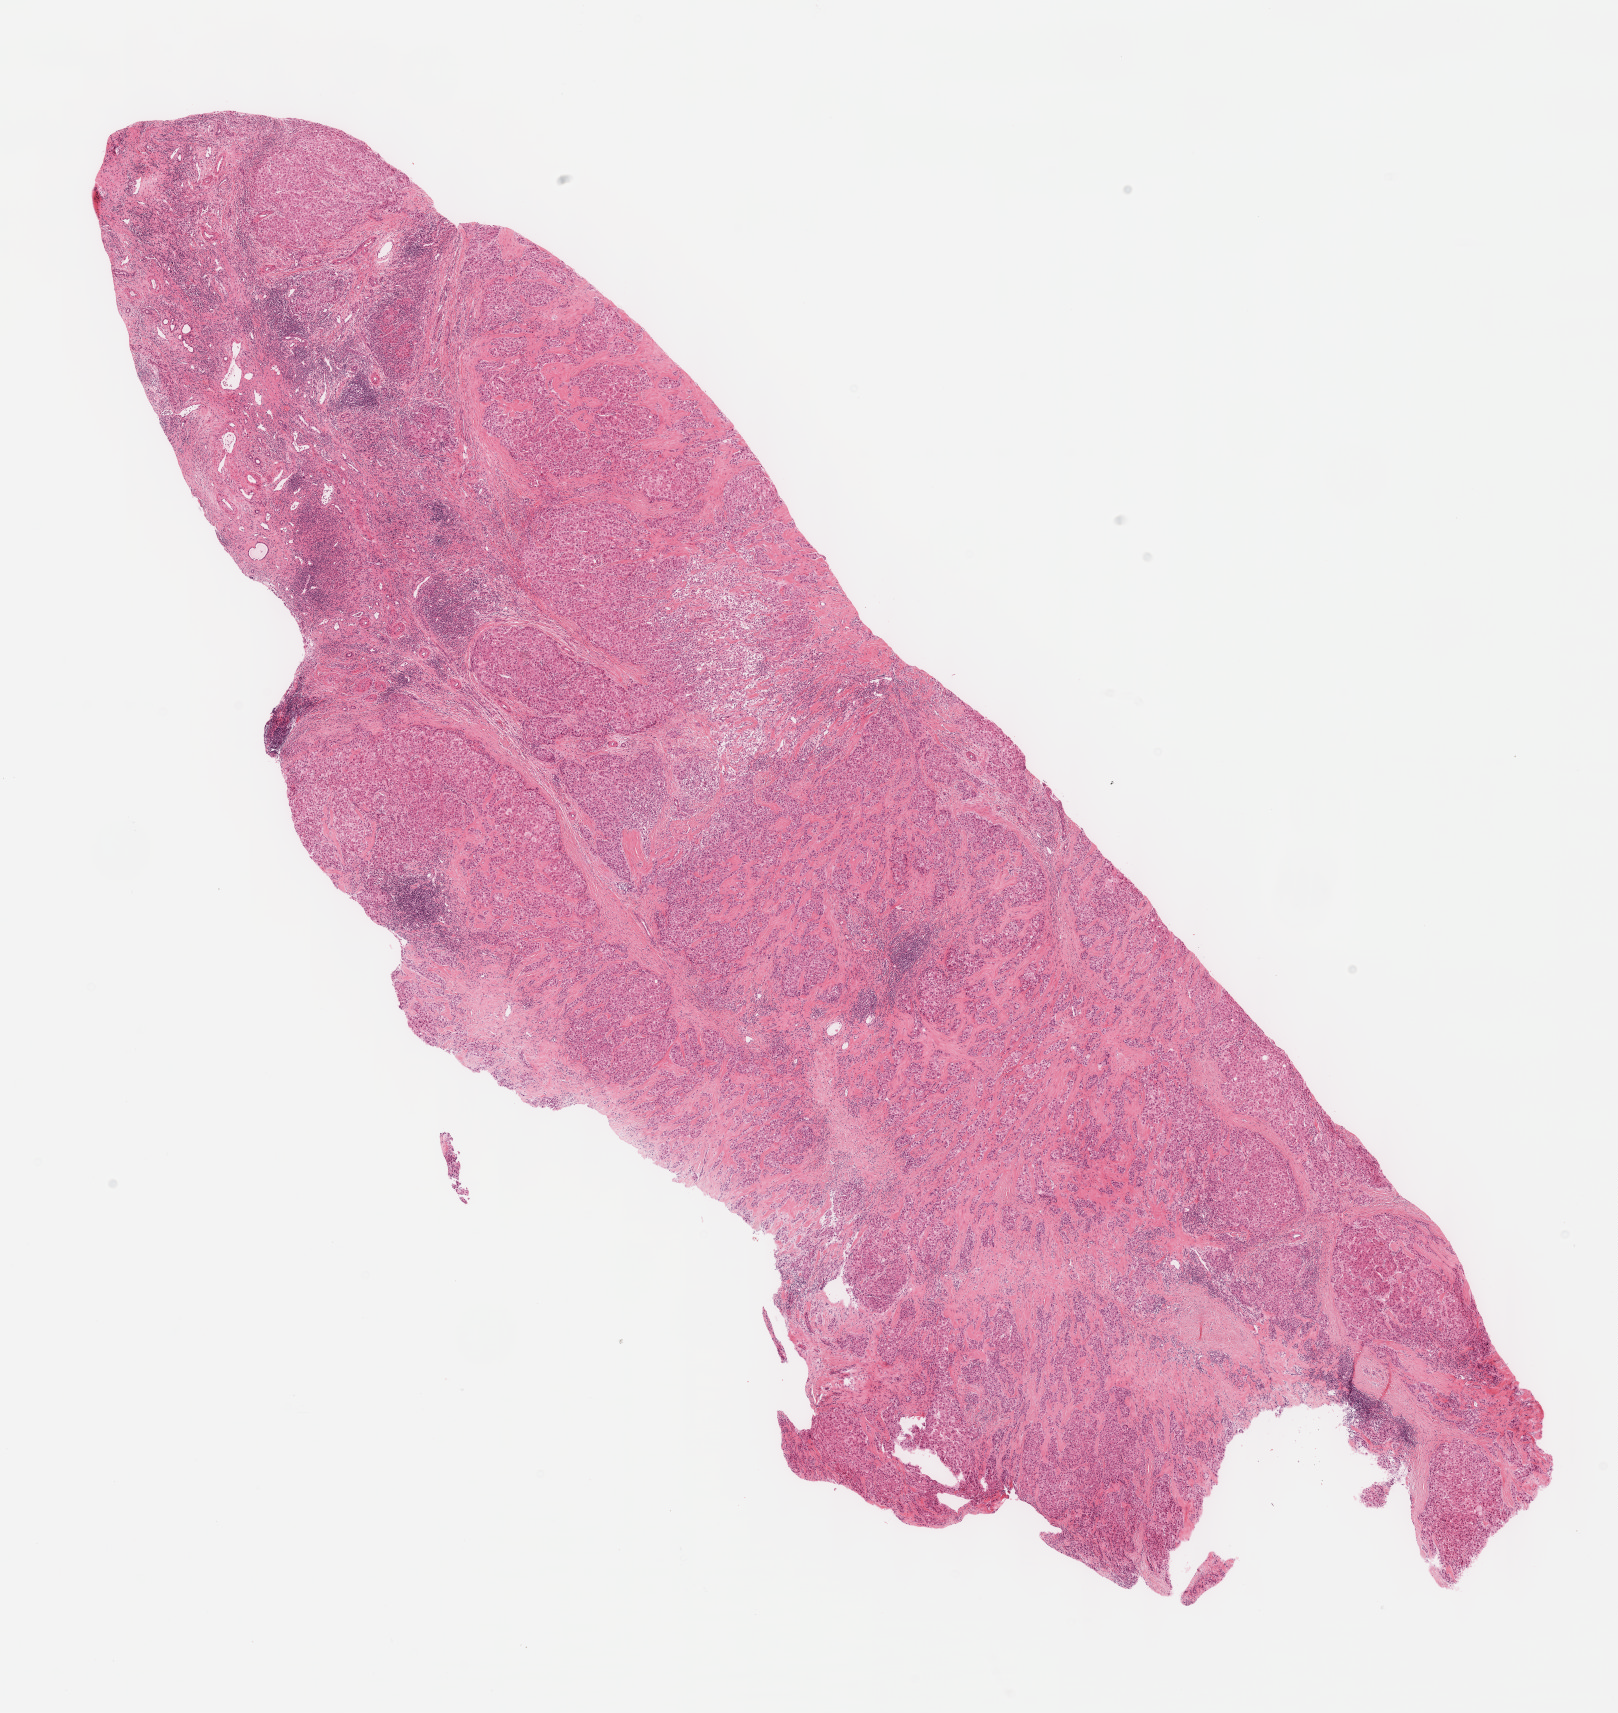
Digitized H&E-stained tissue section (whole slide), whole scanned area (about 13.1 x 13.8 mm, acquisition: 40x scan) shown as a low-resolution overview, formalin-fixed paraffin-embedded (FFPE) diagnostic section, primary tumour sample from the liver. Patient: female, age at initial diagnosis 68 years. Histologic grade: G3 (poorly differentiated).
* pathologic diagnosis: Hepatocellular carcinoma, NOS
* AJCC pathologic stage: II (7th edition)